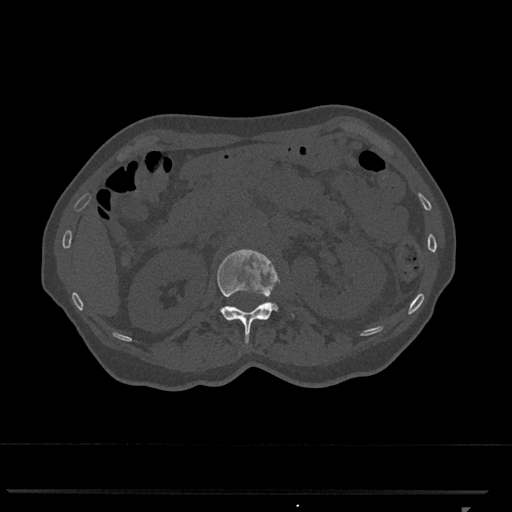
CT including the spine, one axial slice. Position 398 of 793 along the scan axis. Reconstruction kernel Br40s/3. 120 kVp. Bone window (W 1800 / L 400 HU). 0.5 mm slice thickness. 512 × 512 image matrix, field of view 380 × 380 mm. Female patient, age 62 years. From the clinical record (not read from this slice): primary cancer: renal.
Structures marked on this image (semi-automatically segmented with operator editing):
- L1 vertebra: box from (x=217, y=249) to (x=280, y=345) px